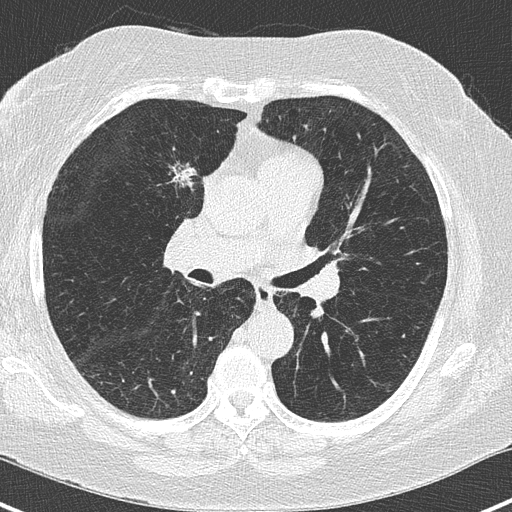
Chest CT (low-dose screening protocol), one axial image; third annual screen; lung window (W 1500 / L -600 HU); 2 mm slice thickness. Female participant, aged 62 years at enrolment.
Expert-annotated lung lesion, box from (x=144, y=145) to (x=215, y=210) px. The screening reader recorded 4 non-calcified nodules or masses ≥4 mm on this exam (right upper lobe, left lower lobe, left lower lobe); which of them this box marks is not recorded. Official screen result: positive, other. Participant outcome: lung cancer diagnosed 41 days after this screen — adenocarcinoma, NOS, right upper lobe, moderately differentiated (G2), stage IA (AJCC 6th edition), 15 mm at pathology.